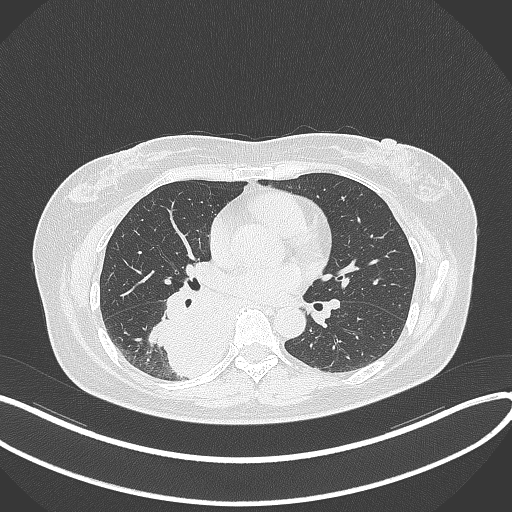
Chest CT, one axial slice; position 179 of 331 along the scan axis; lung window (W 1500 / L -600 HU); 1 mm slice thickness; 512 × 512 image matrix, field of view 400 × 400 mm. Patient: female, 54 years. From the clinical record (not read from this slice): clinical TNM (as recorded): T4 N0 M0.
Structures marked on this image (rectangle marked by the reading radiologist):
- lung tumour (recorded histology: adenocarcinoma): bounding box [x1, y1, x2, y2] px = [152, 287, 241, 382]